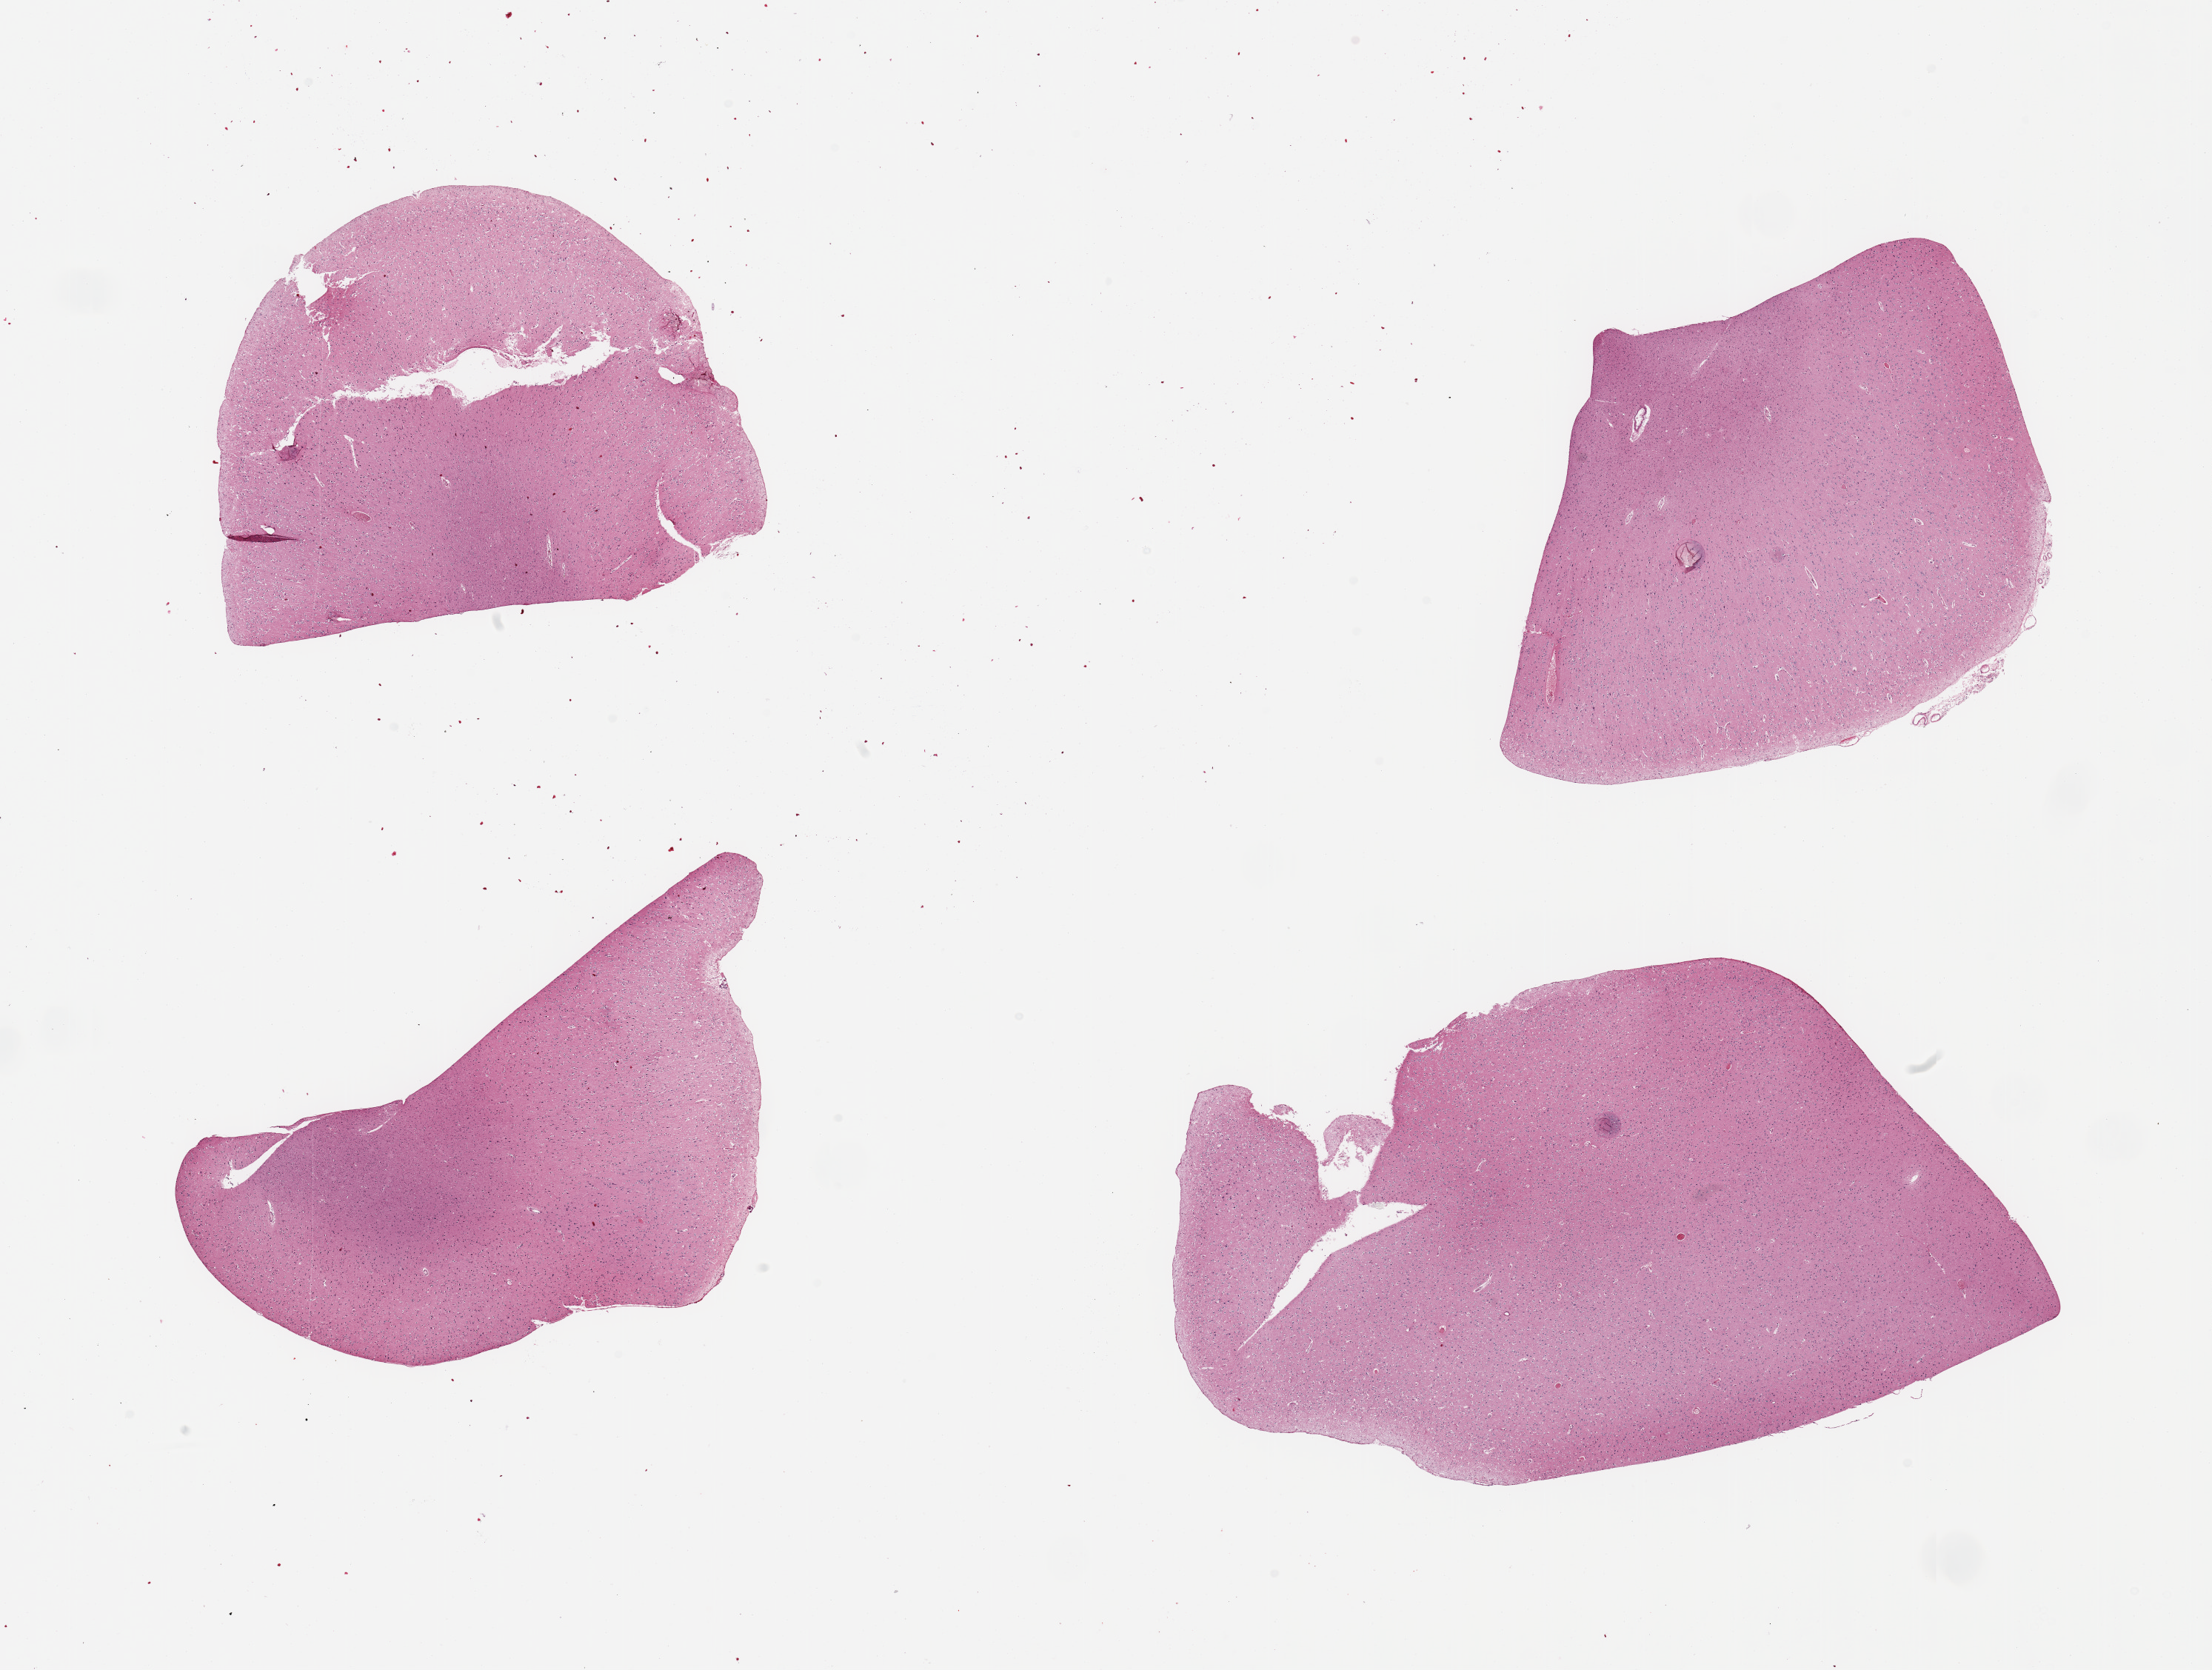
Whole-slide image, hematoxylin and eosin (H&E) stain, brightfield, whole scanned area (about 23.6 x 17.8 mm) shown as a low-resolution overview, PAXgene-fixed, paraffin-embedded tissue, section of cerebral cortex (target tissue), donor tissue sample. Donor: male.
* review note (as recorded): 4 pieces; well sampled cortex